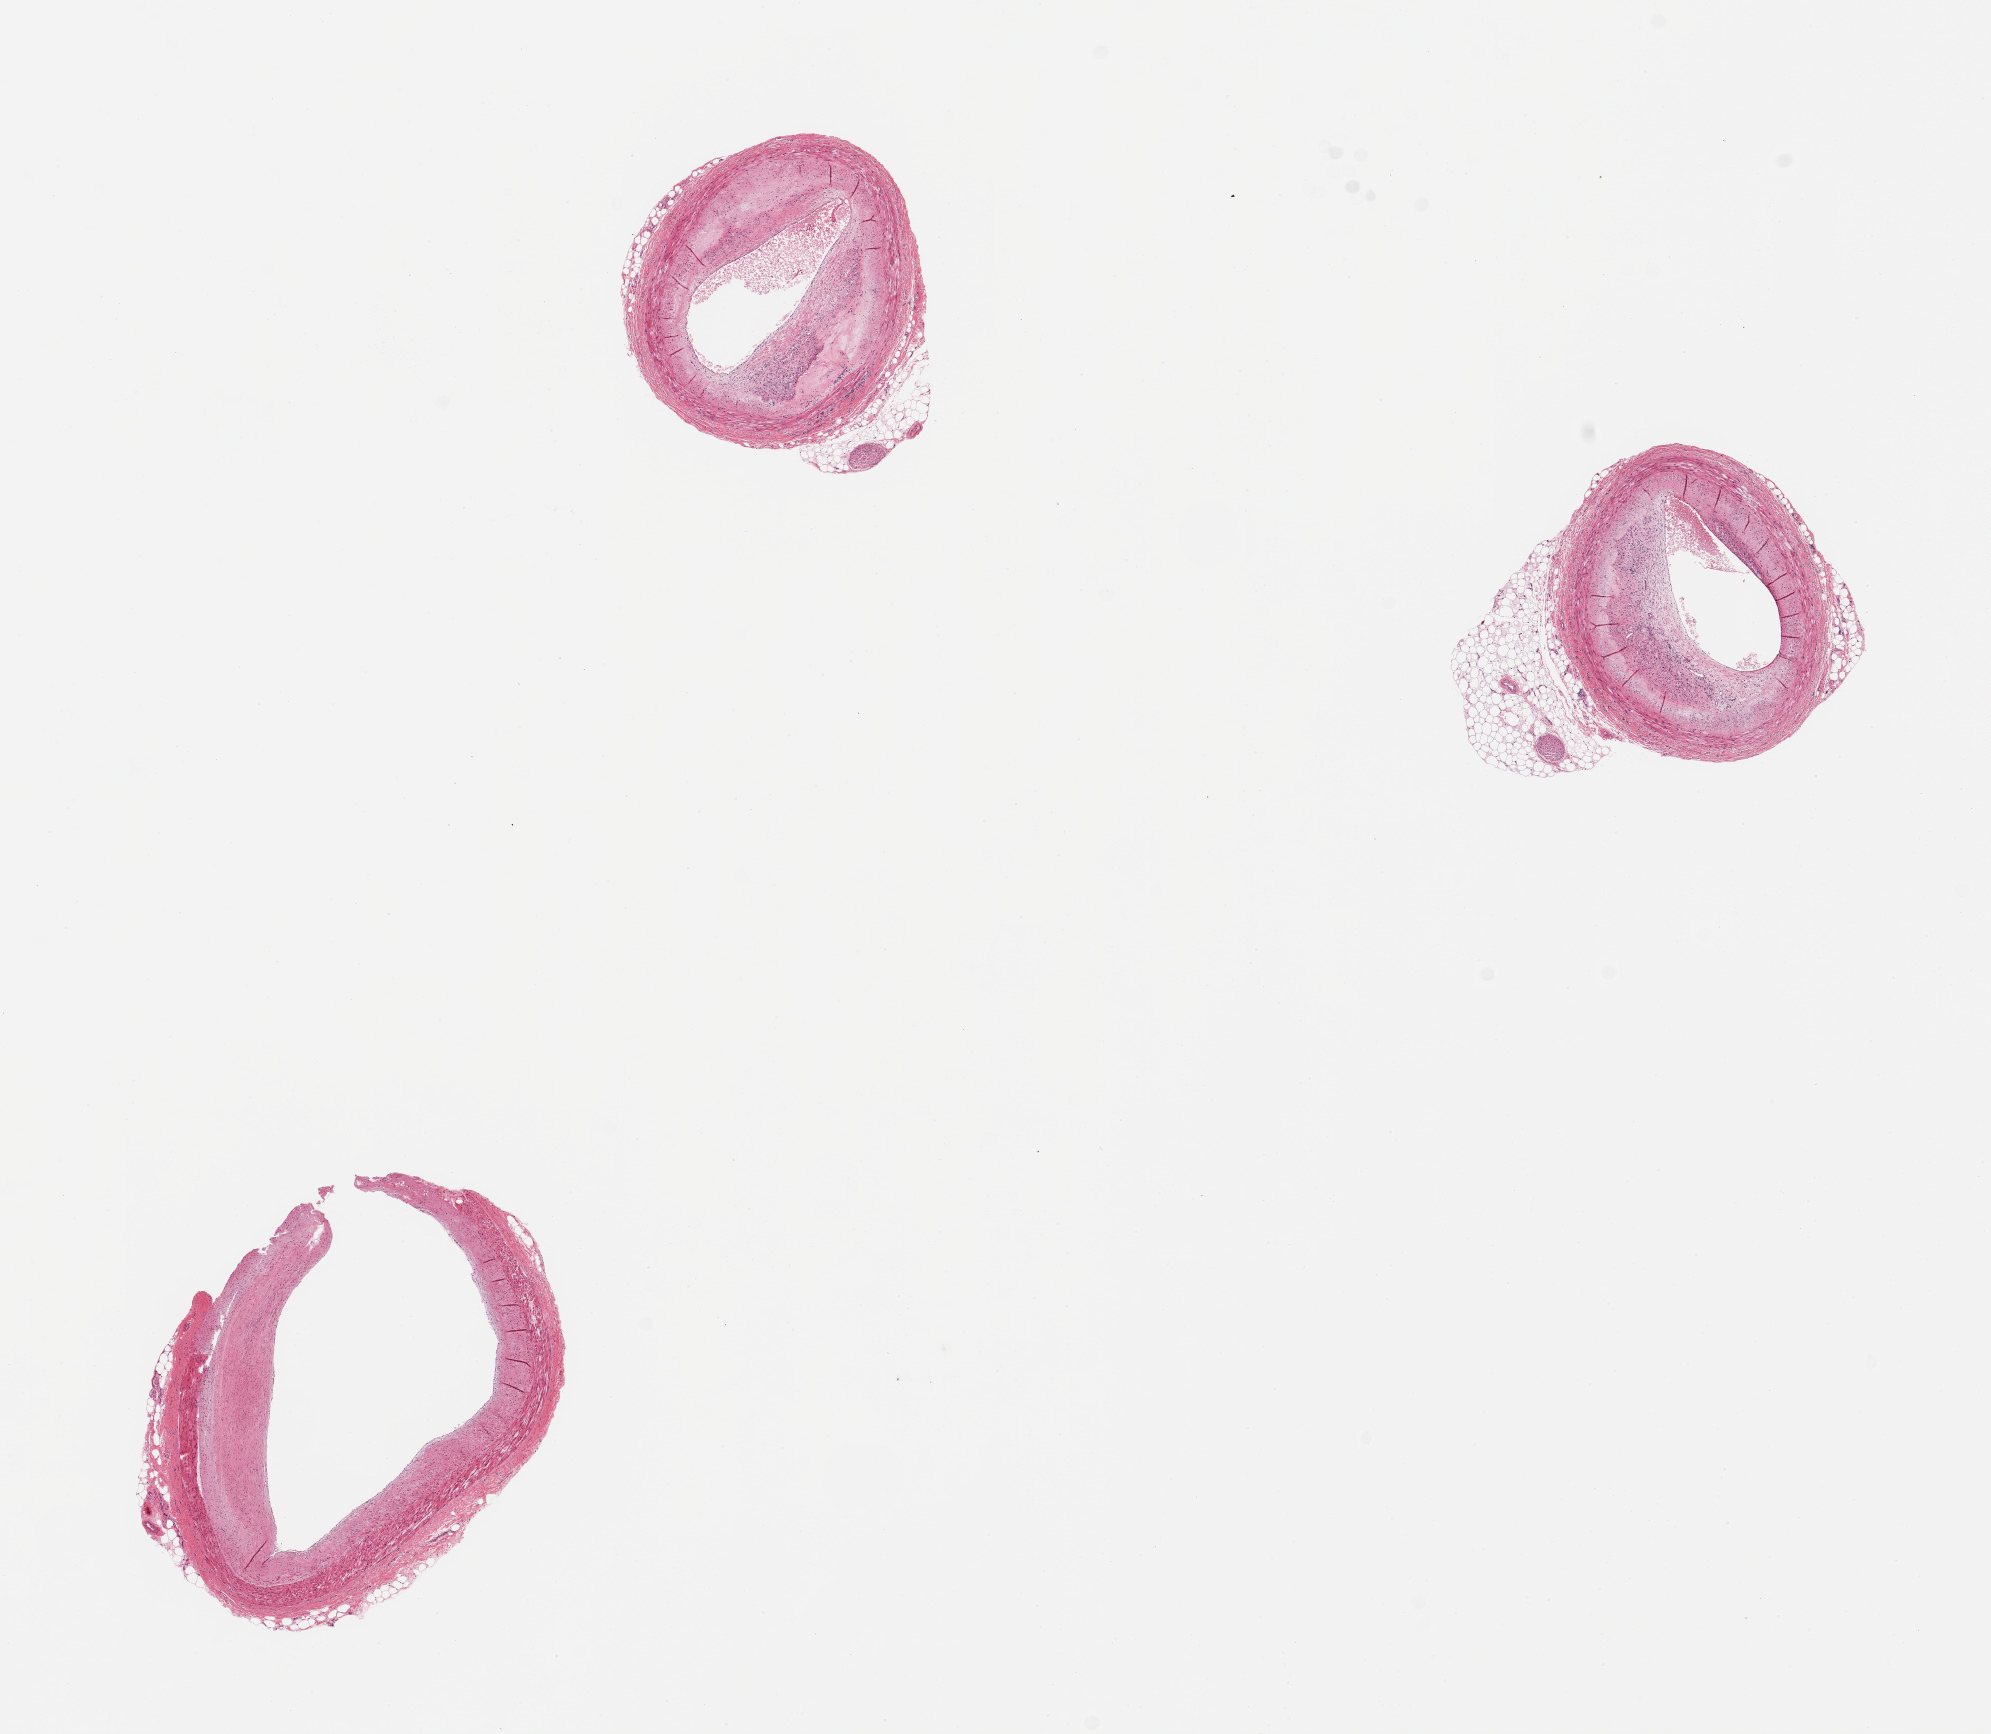
Whole-slide image, H&E stain, brightfield — whole scanned area (about 15.8 x 13.7 mm) shown as a low-resolution overview, PAXgene-fixed, paraffin-embedded tissue, sampled site (target tissue): coronary artery, tissue donor sample.
* pathologist's review note for this sample: 3 pieces, ~50% occlusive atherosis; nubbin of adherent fat, ~1mm